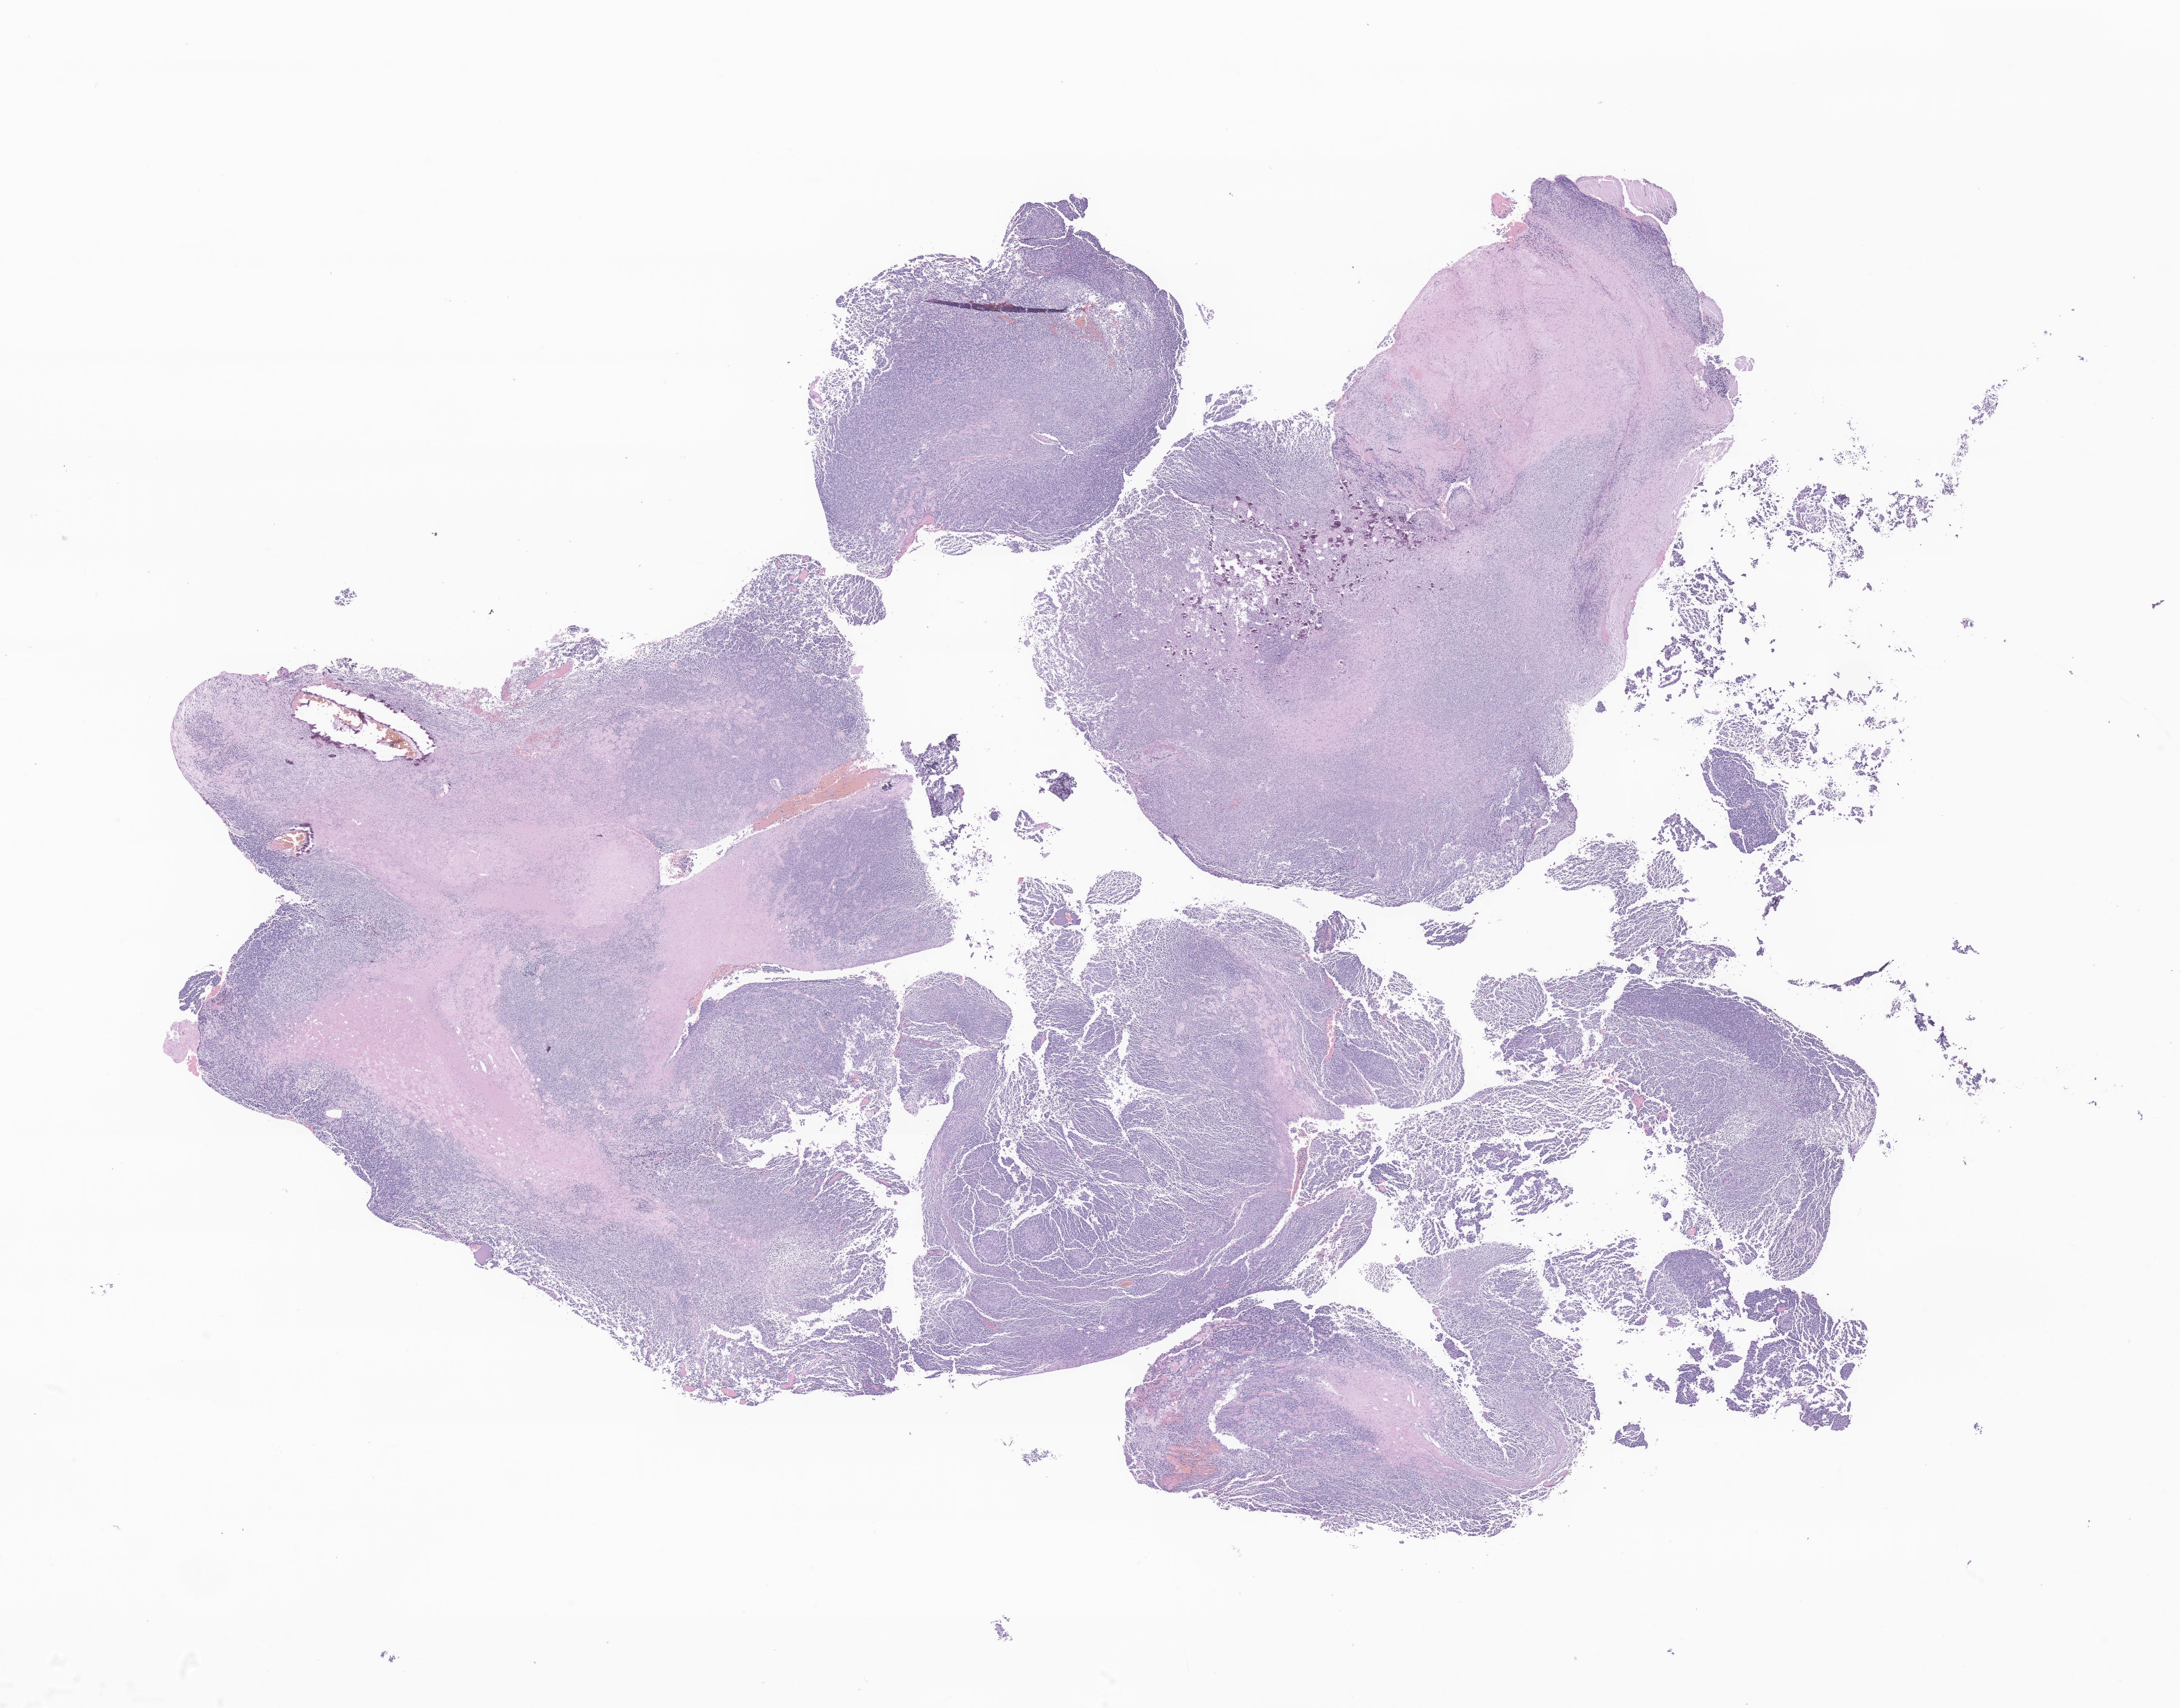
H&E whole-slide image of tumor tissue from the brain — shown as a low-resolution overview of the whole scanned area (about 24.1 x 18.9 mm); formalin-fixed, paraffin-embedded (FFPE) tissue. Patient: male, age 132 months (11 years).
- recorded diagnosis: Medulloblastoma, NOS